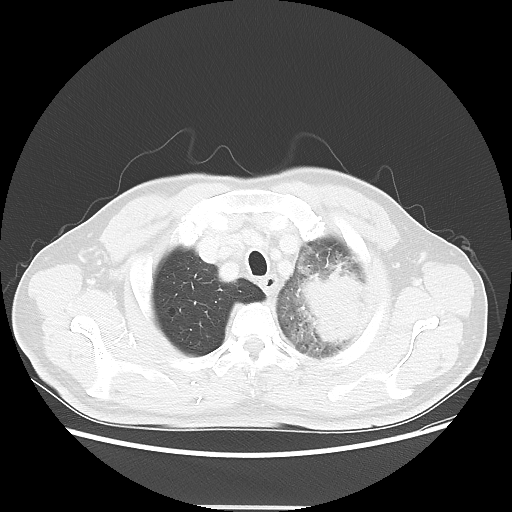
Chest CT, one axial slice. Reconstruction kernel LUNG. 100 kVp. Lung window (W 1500 / L -600 HU). 5 mm slice thickness. 512 × 512 image matrix, field of view 391 × 391 mm. Male patient, age 60 years. From the clinical record (not read from this slice): clinical TNM (as recorded): T4 N1 M1a; histopathological grade: G3.
Structures marked on this image (bounding box drawn by a radiologist):
- lung tumour (recorded histology: large cell carcinoma): bounding box [x1, y1, x2, y2] px = [291, 261, 370, 348]